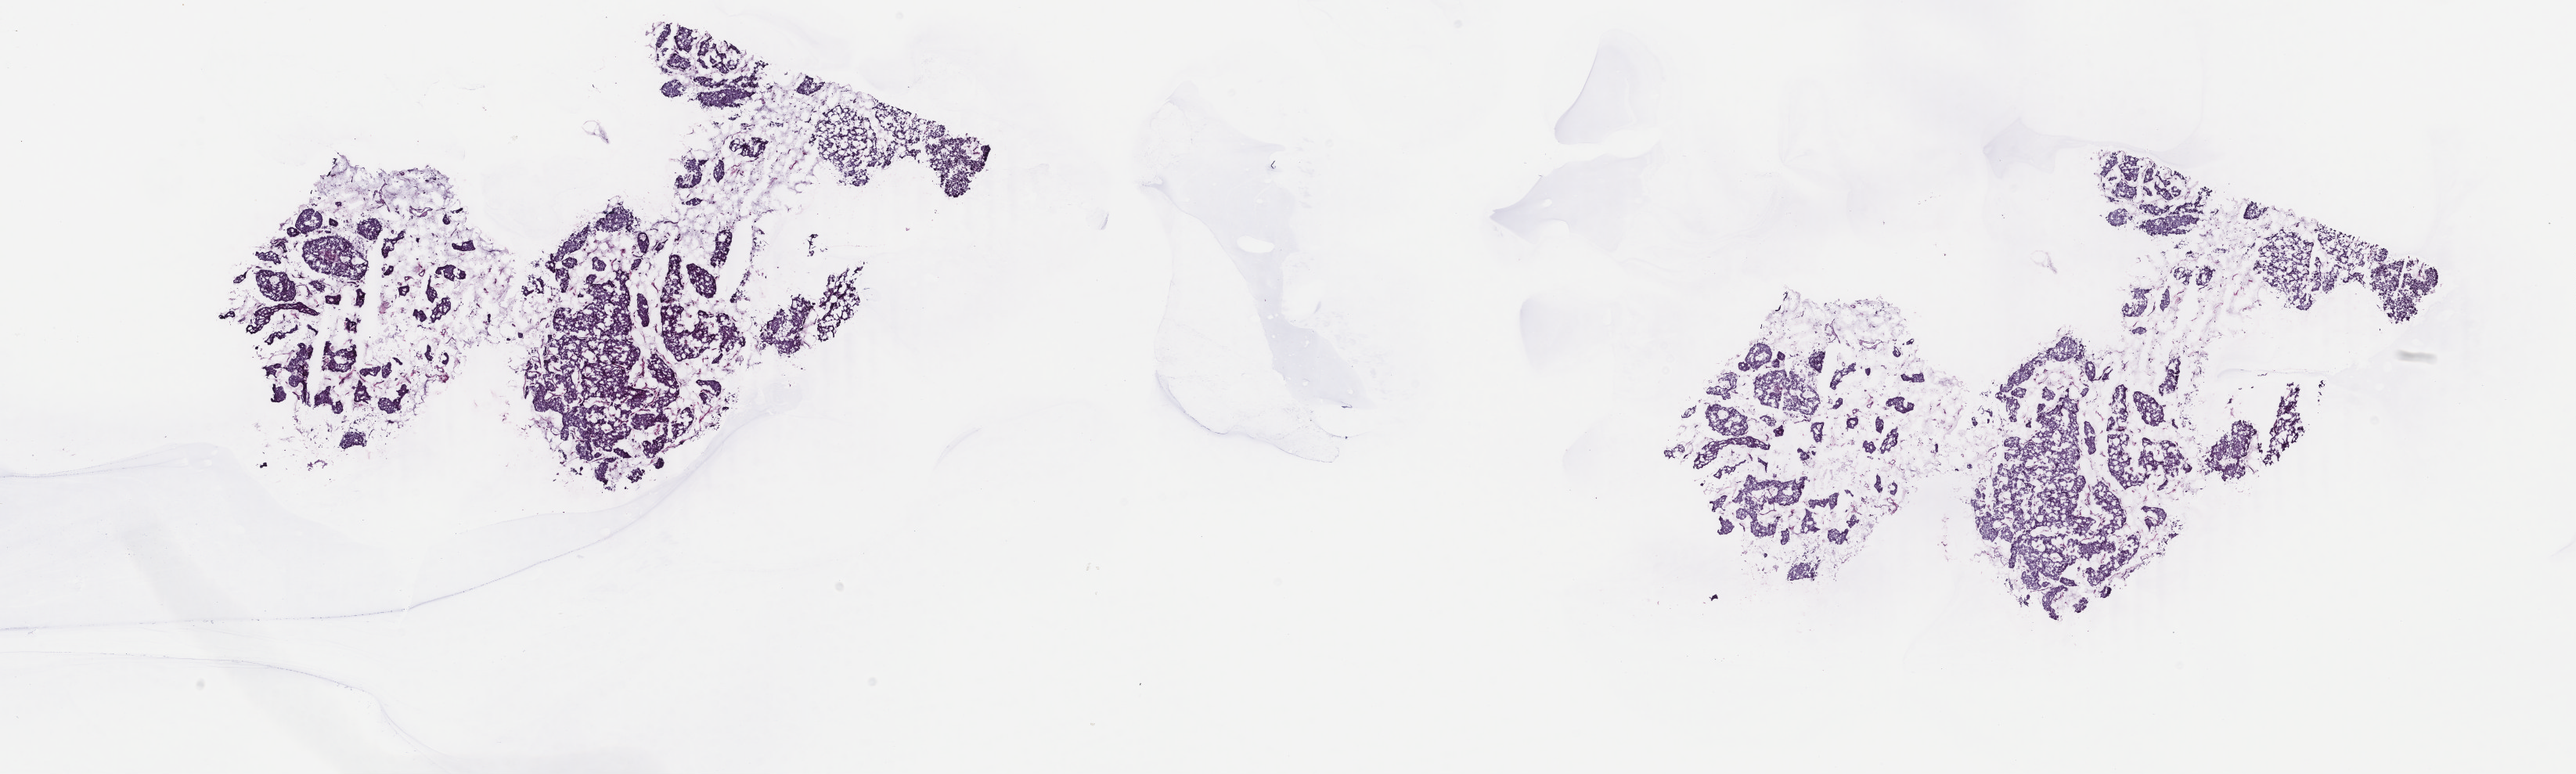
Digitized H&E tissue section (whole slide), a low-resolution overview of the entire scanned area, about 26.2 x 7.9 mm (from a 40x scan); frozen section; primary tumour sample from the breast. Patient: female, age at initial diagnosis 69 years. Pathologist review of this section (percent, as recorded): tumour cells 100%, tumour nuclei 98%, normal cells 0%, stromal cells 0%, necrosis 0%. Inflammatory infiltration, as recorded: lymphocyte infiltration 0%, monocyte infiltration 0%, neutrophil infiltration 0%.
• pathologic diagnosis: Infiltrating duct mixed with other types of carcinoma
• lymph nodes positive (case pathology): 0 of 10 examined
• AJCC pathologic stage: IIA (6th edition)